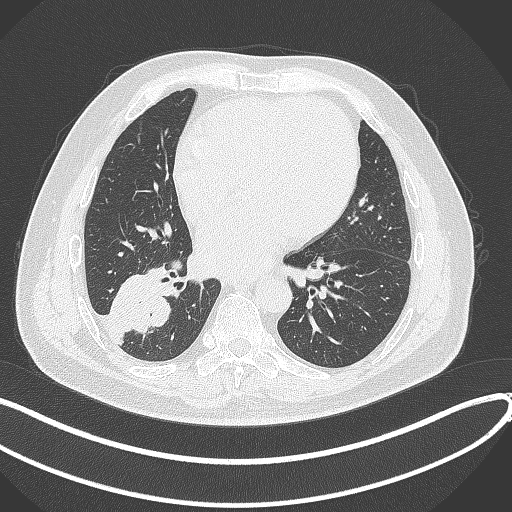
Chest CT, one axial slice; position 149 of 360 along the scan axis; reconstruction kernel B70f; lung window (W 1500 / L -600 HU); 1 mm slice thickness; 512 × 512 image matrix. Patient: male, 59 years.
Outlined on this slice (rectangle marked by the reading radiologist):
- lung tumour (recorded histology: adenocarcinoma): bounding box <105,268,173,332> (left, top, right, bottom; pixels)